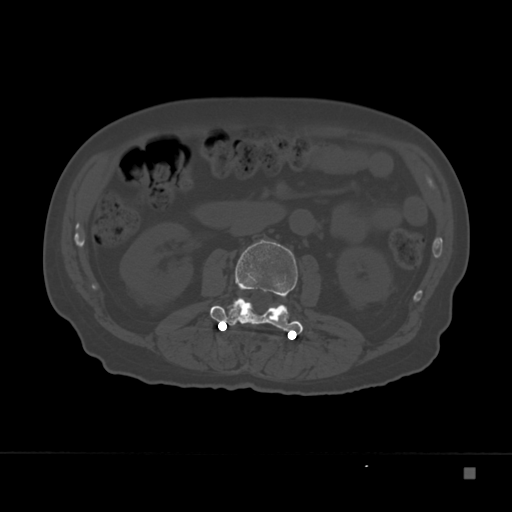
CT including the spine, one axial slice; position 86 of 332 along the scan axis; 120 kVp; bone window (W 1800 / L 400 HU); 1.5 mm slice thickness; 512 × 512 image matrix, field of view 389 × 389 mm. Male patient, age 72 years. From the clinical record (not read from this slice): primary cancer: skeletal.
Outlined on this slice (semi-automatically segmented with operator editing):
- L2 vertebra: bounding box [x1, y1, x2, y2] px = [211, 239, 303, 335]
- L3 vertebra: [226, 321, 298, 332]